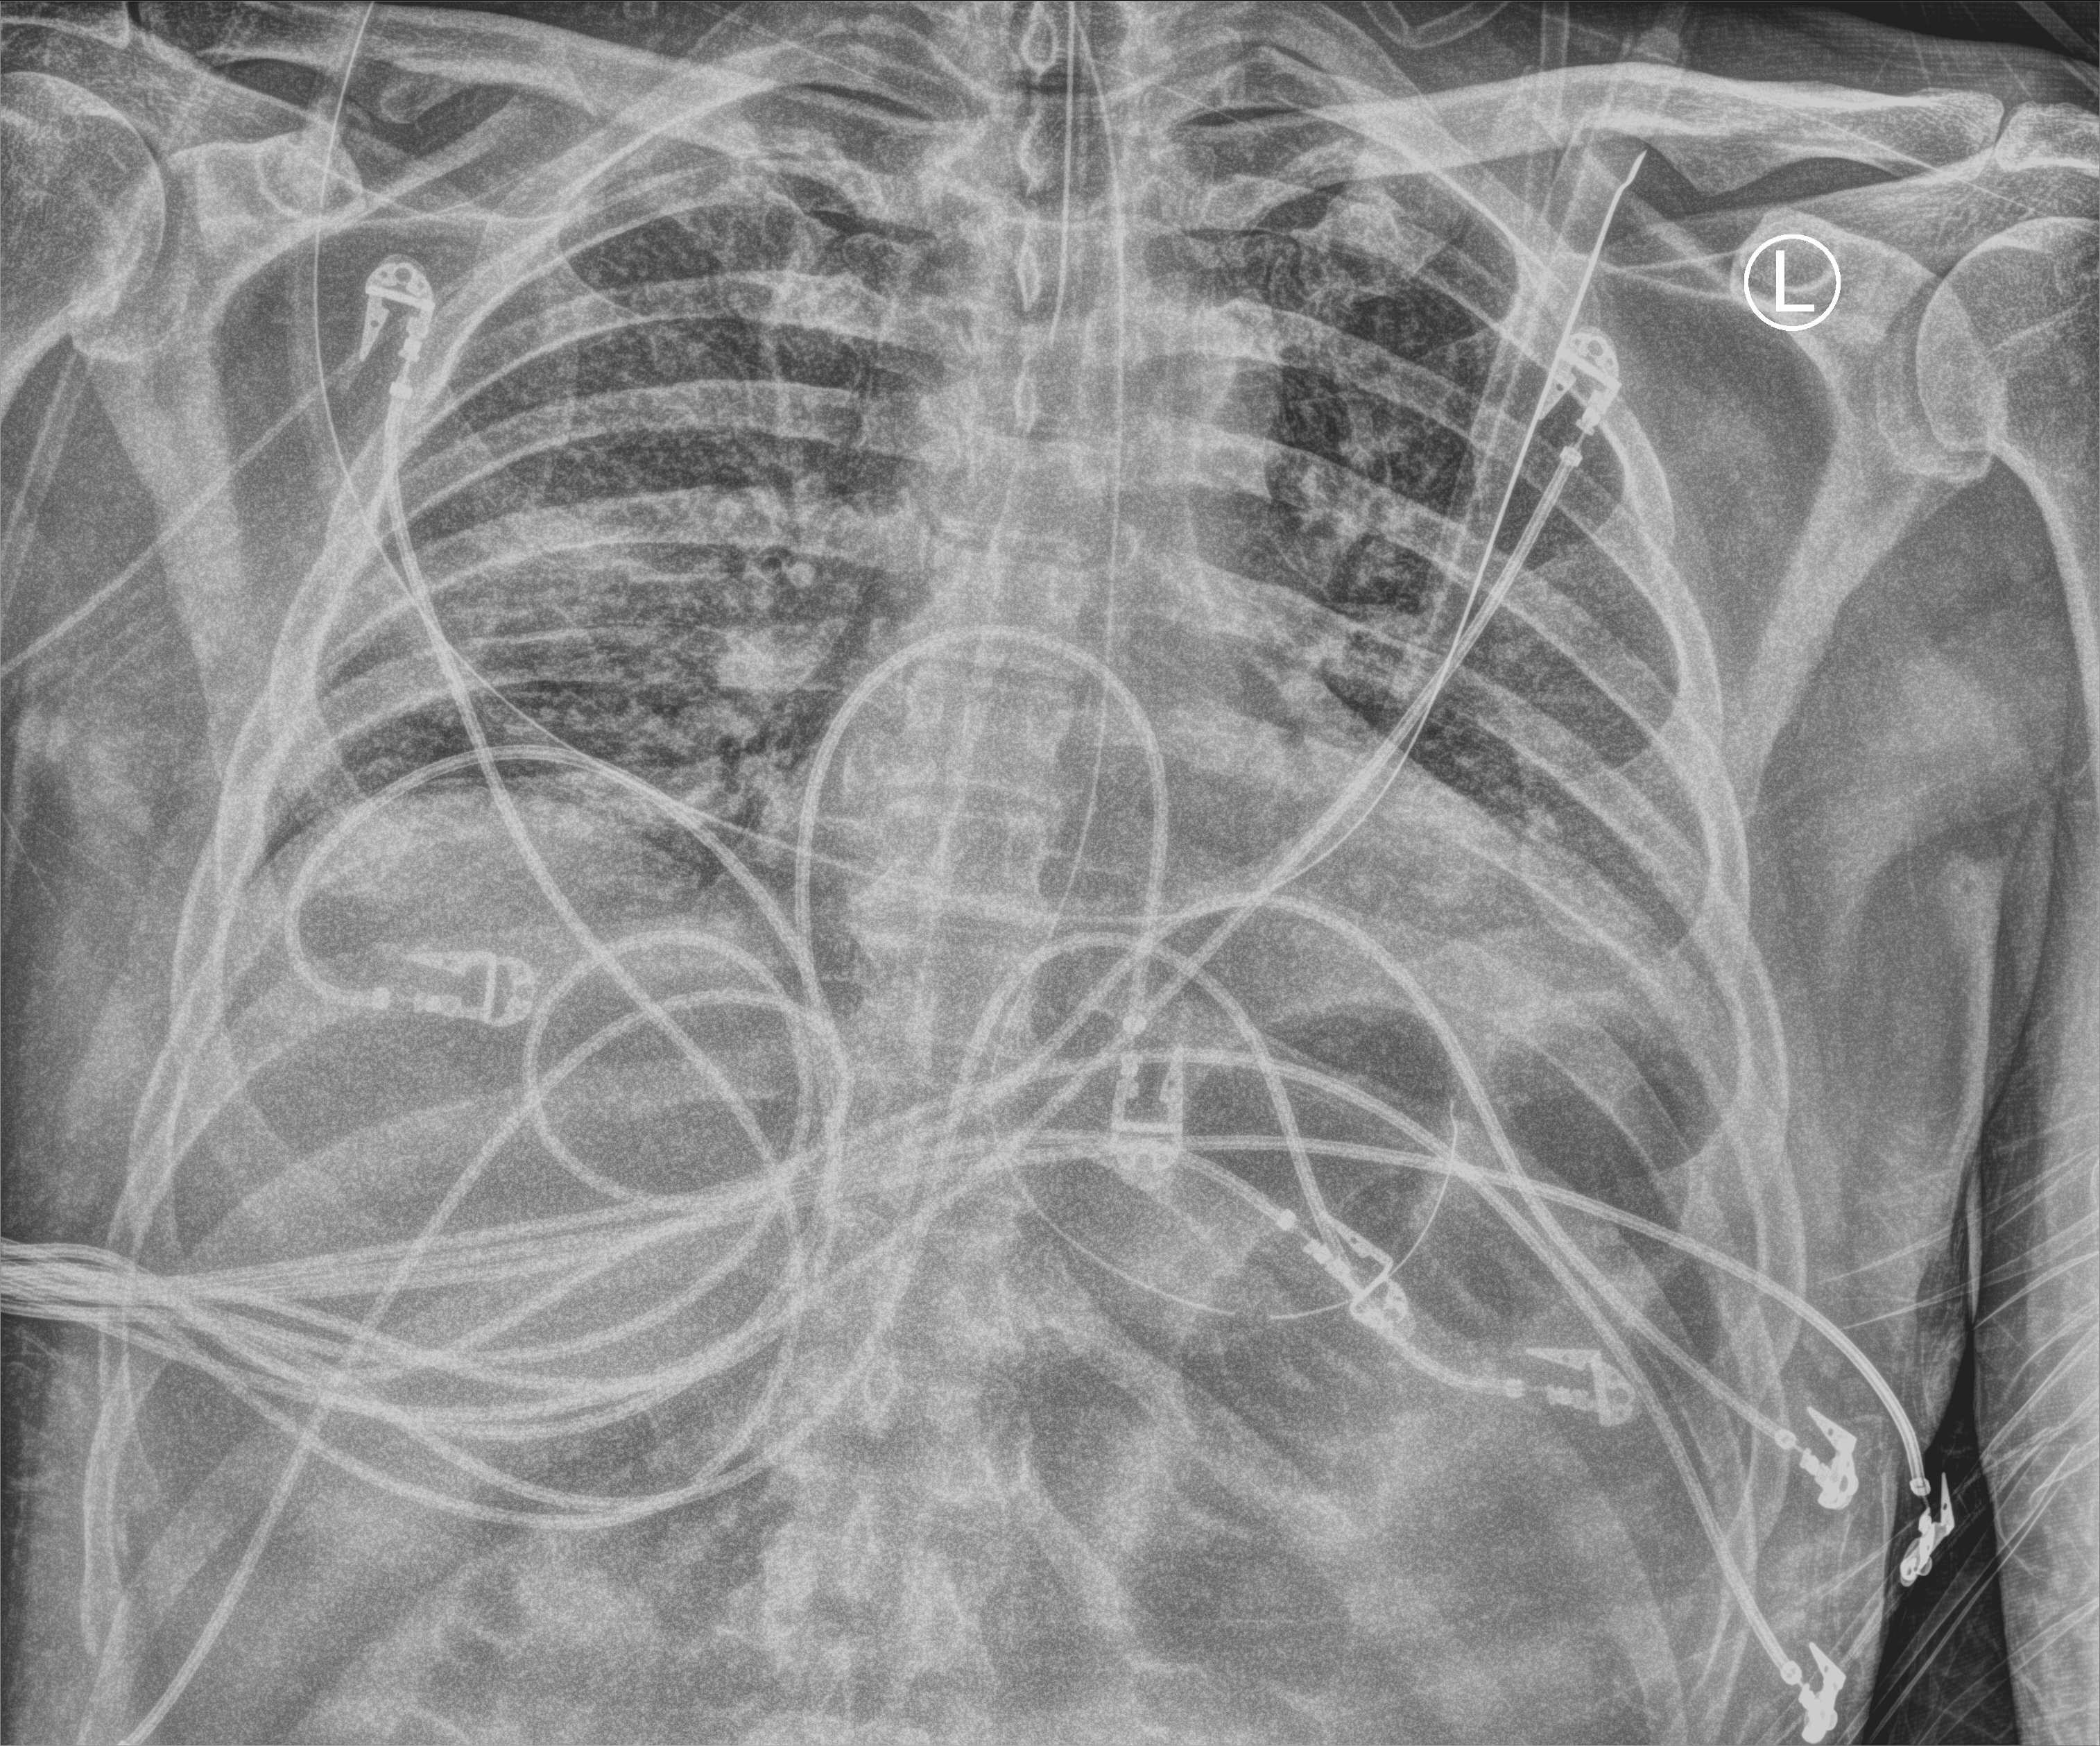
Bedside chest radiograph (computed radiography). Patient hospitalised with COVID-19; male, aged 60–74 years.
Admission-level facts for this patient (not findings on this image; timing relative to this image not recorded): admitted to intensive care during this hospital stay: yes; mechanically ventilated during this hospital stay: yes; diabetes (admission record): yes.